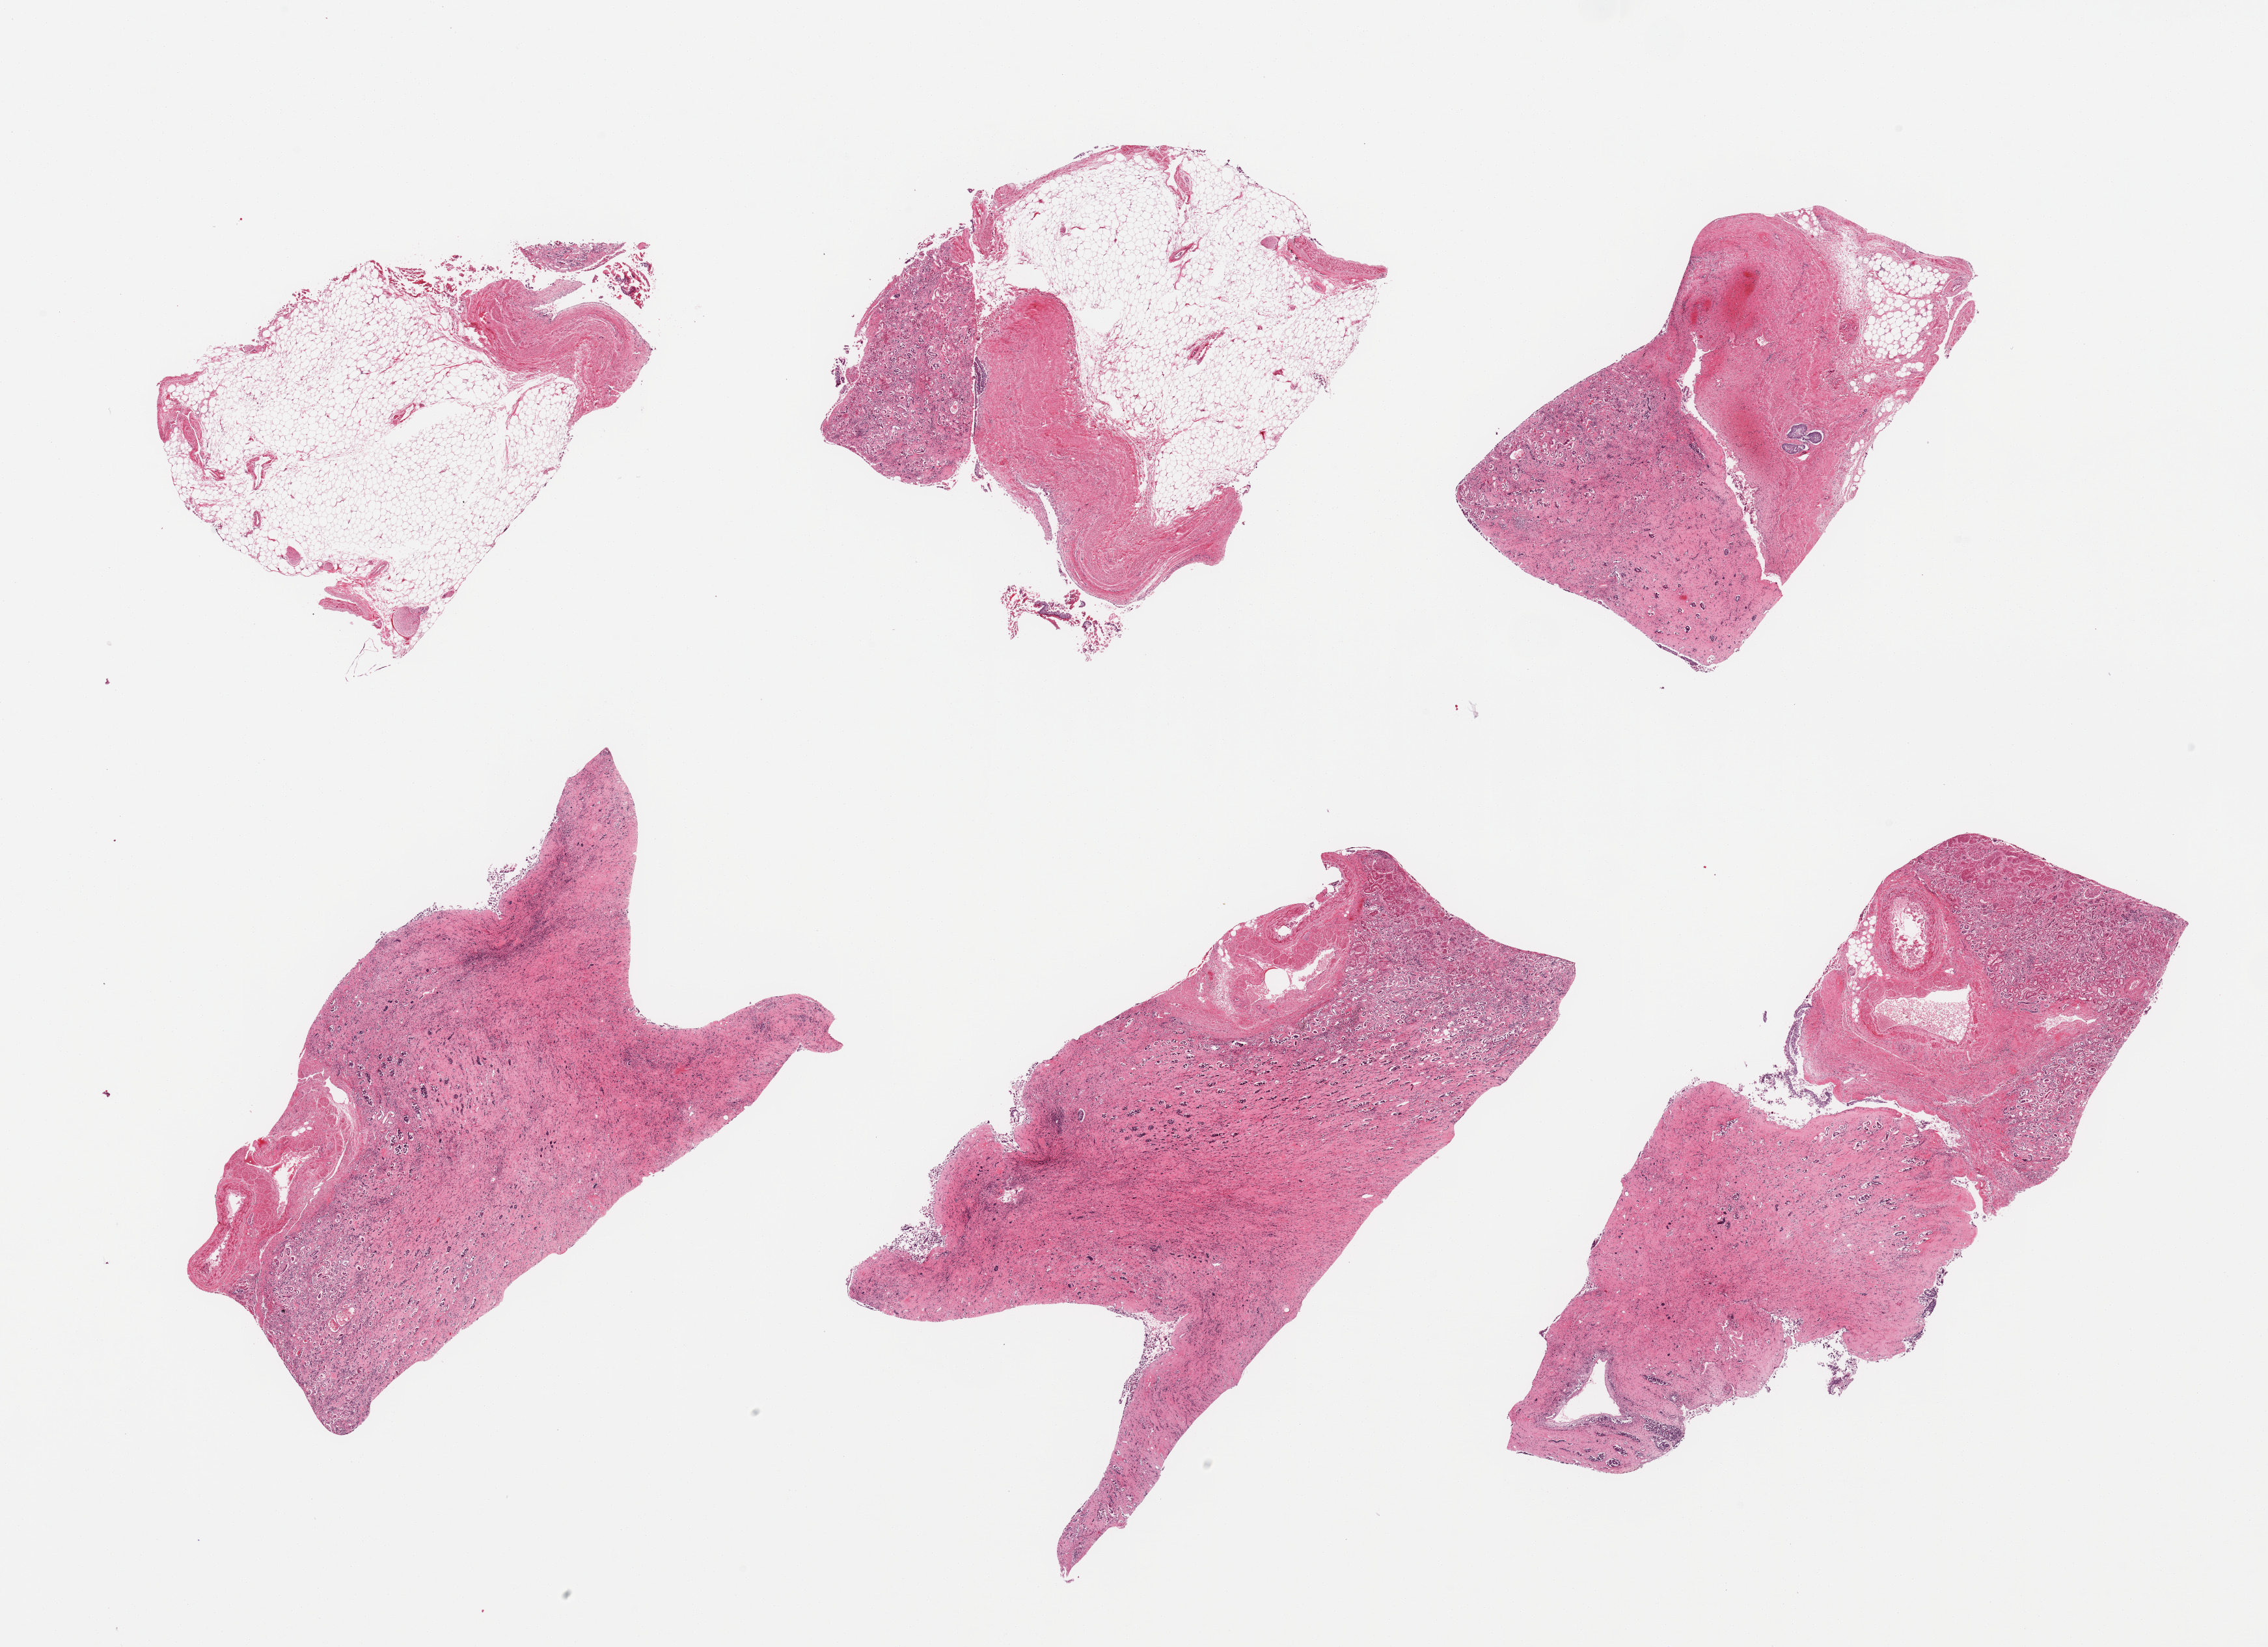
Whole-slide image, hematoxylin and eosin (H&E) stain, a low-resolution overview of the entire scanned area, about 27.6 x 20.0 mm (slide scanned at 20x). PAXgene-fixed, paraffin-embedded tissue. Sampled site (target tissue): renal cortex. Tissue donor sample.
Reviewer comment on this tissue sample: 6 pieces, no cortex, renal hilar elements including tubules, urothelium, vascular elements, hilar fat (~40%).